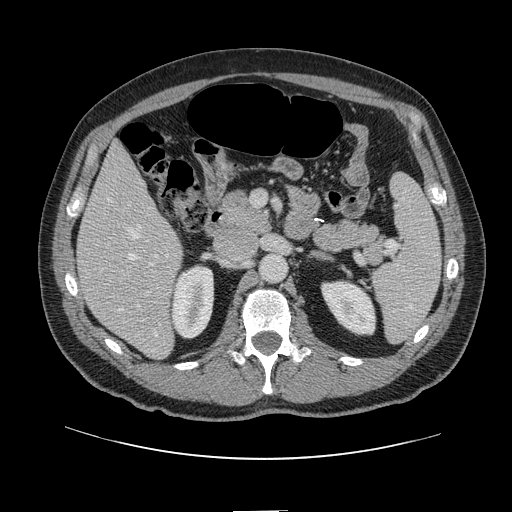
Contrast-enhanced abdominal CT, one axial slice. Slice 57 of 161 in the series (ordered by position). 120 kVp. Soft-tissue window (W 400 / L 40 HU). 512 × 512 image matrix, field of view 412 × 412 mm. Male patient, age 66 years. From the clinical record (not read from this slice): diagnosis: colorectal cancer liver metastases, imaged before liver resection; multiple liver metastases: no; largest metastasis: 3.5 cm; disease in both lobes: no.
Annotated regions visible in this slice (manually delineated by an expert):
- hepatic veins: bounding box <109,200,158,336> (left, top, right, bottom; pixels)
- liver: <78,144,182,358>
- planned liver remnant (the part of the liver to remain after resection): <78,144,168,281>
- portal vein (with intrahepatic branches): <145,254,159,296>